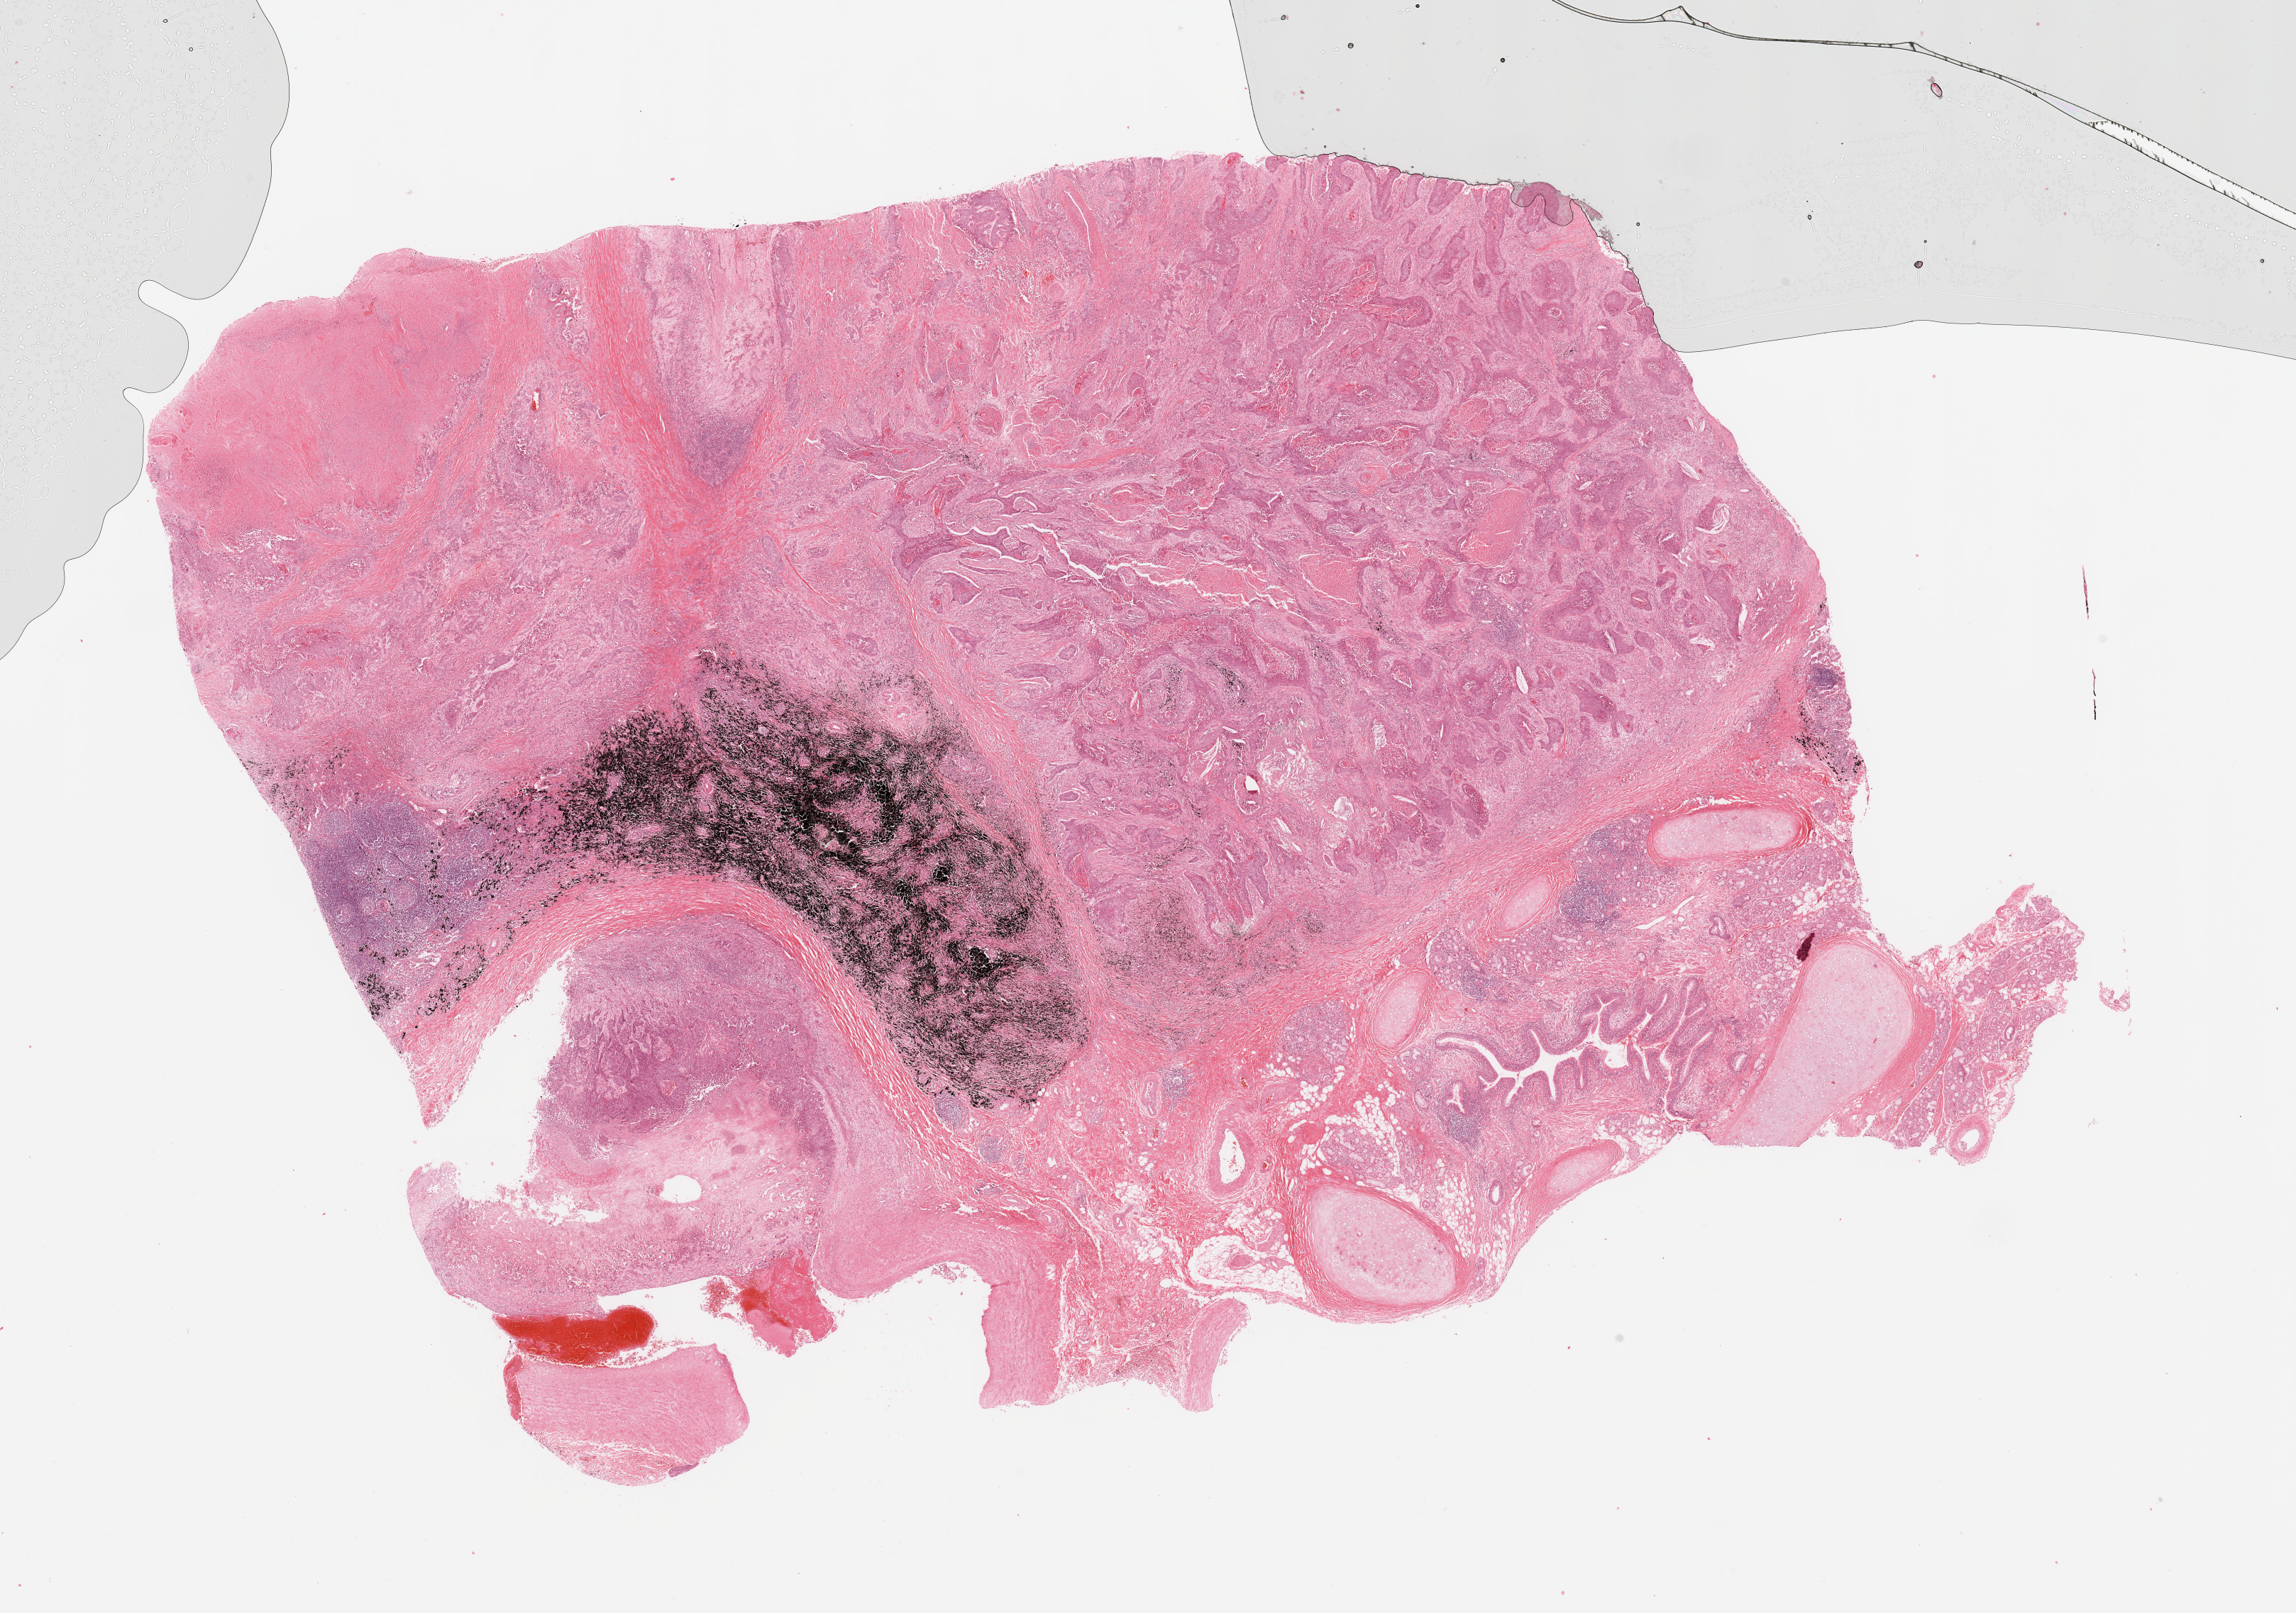
H&E whole-slide image, a low-resolution overview of the entire scanned area, about 25.6 x 18.0 mm (acquisition: 20x scan), lung, tumour tissue. Patient: male, age 72 years. Histologic grade: G3 (poorly differentiated).
Histologic diagnosis: Squamous cell carcinoma, NOS. AJCC pathologic stage: IB.